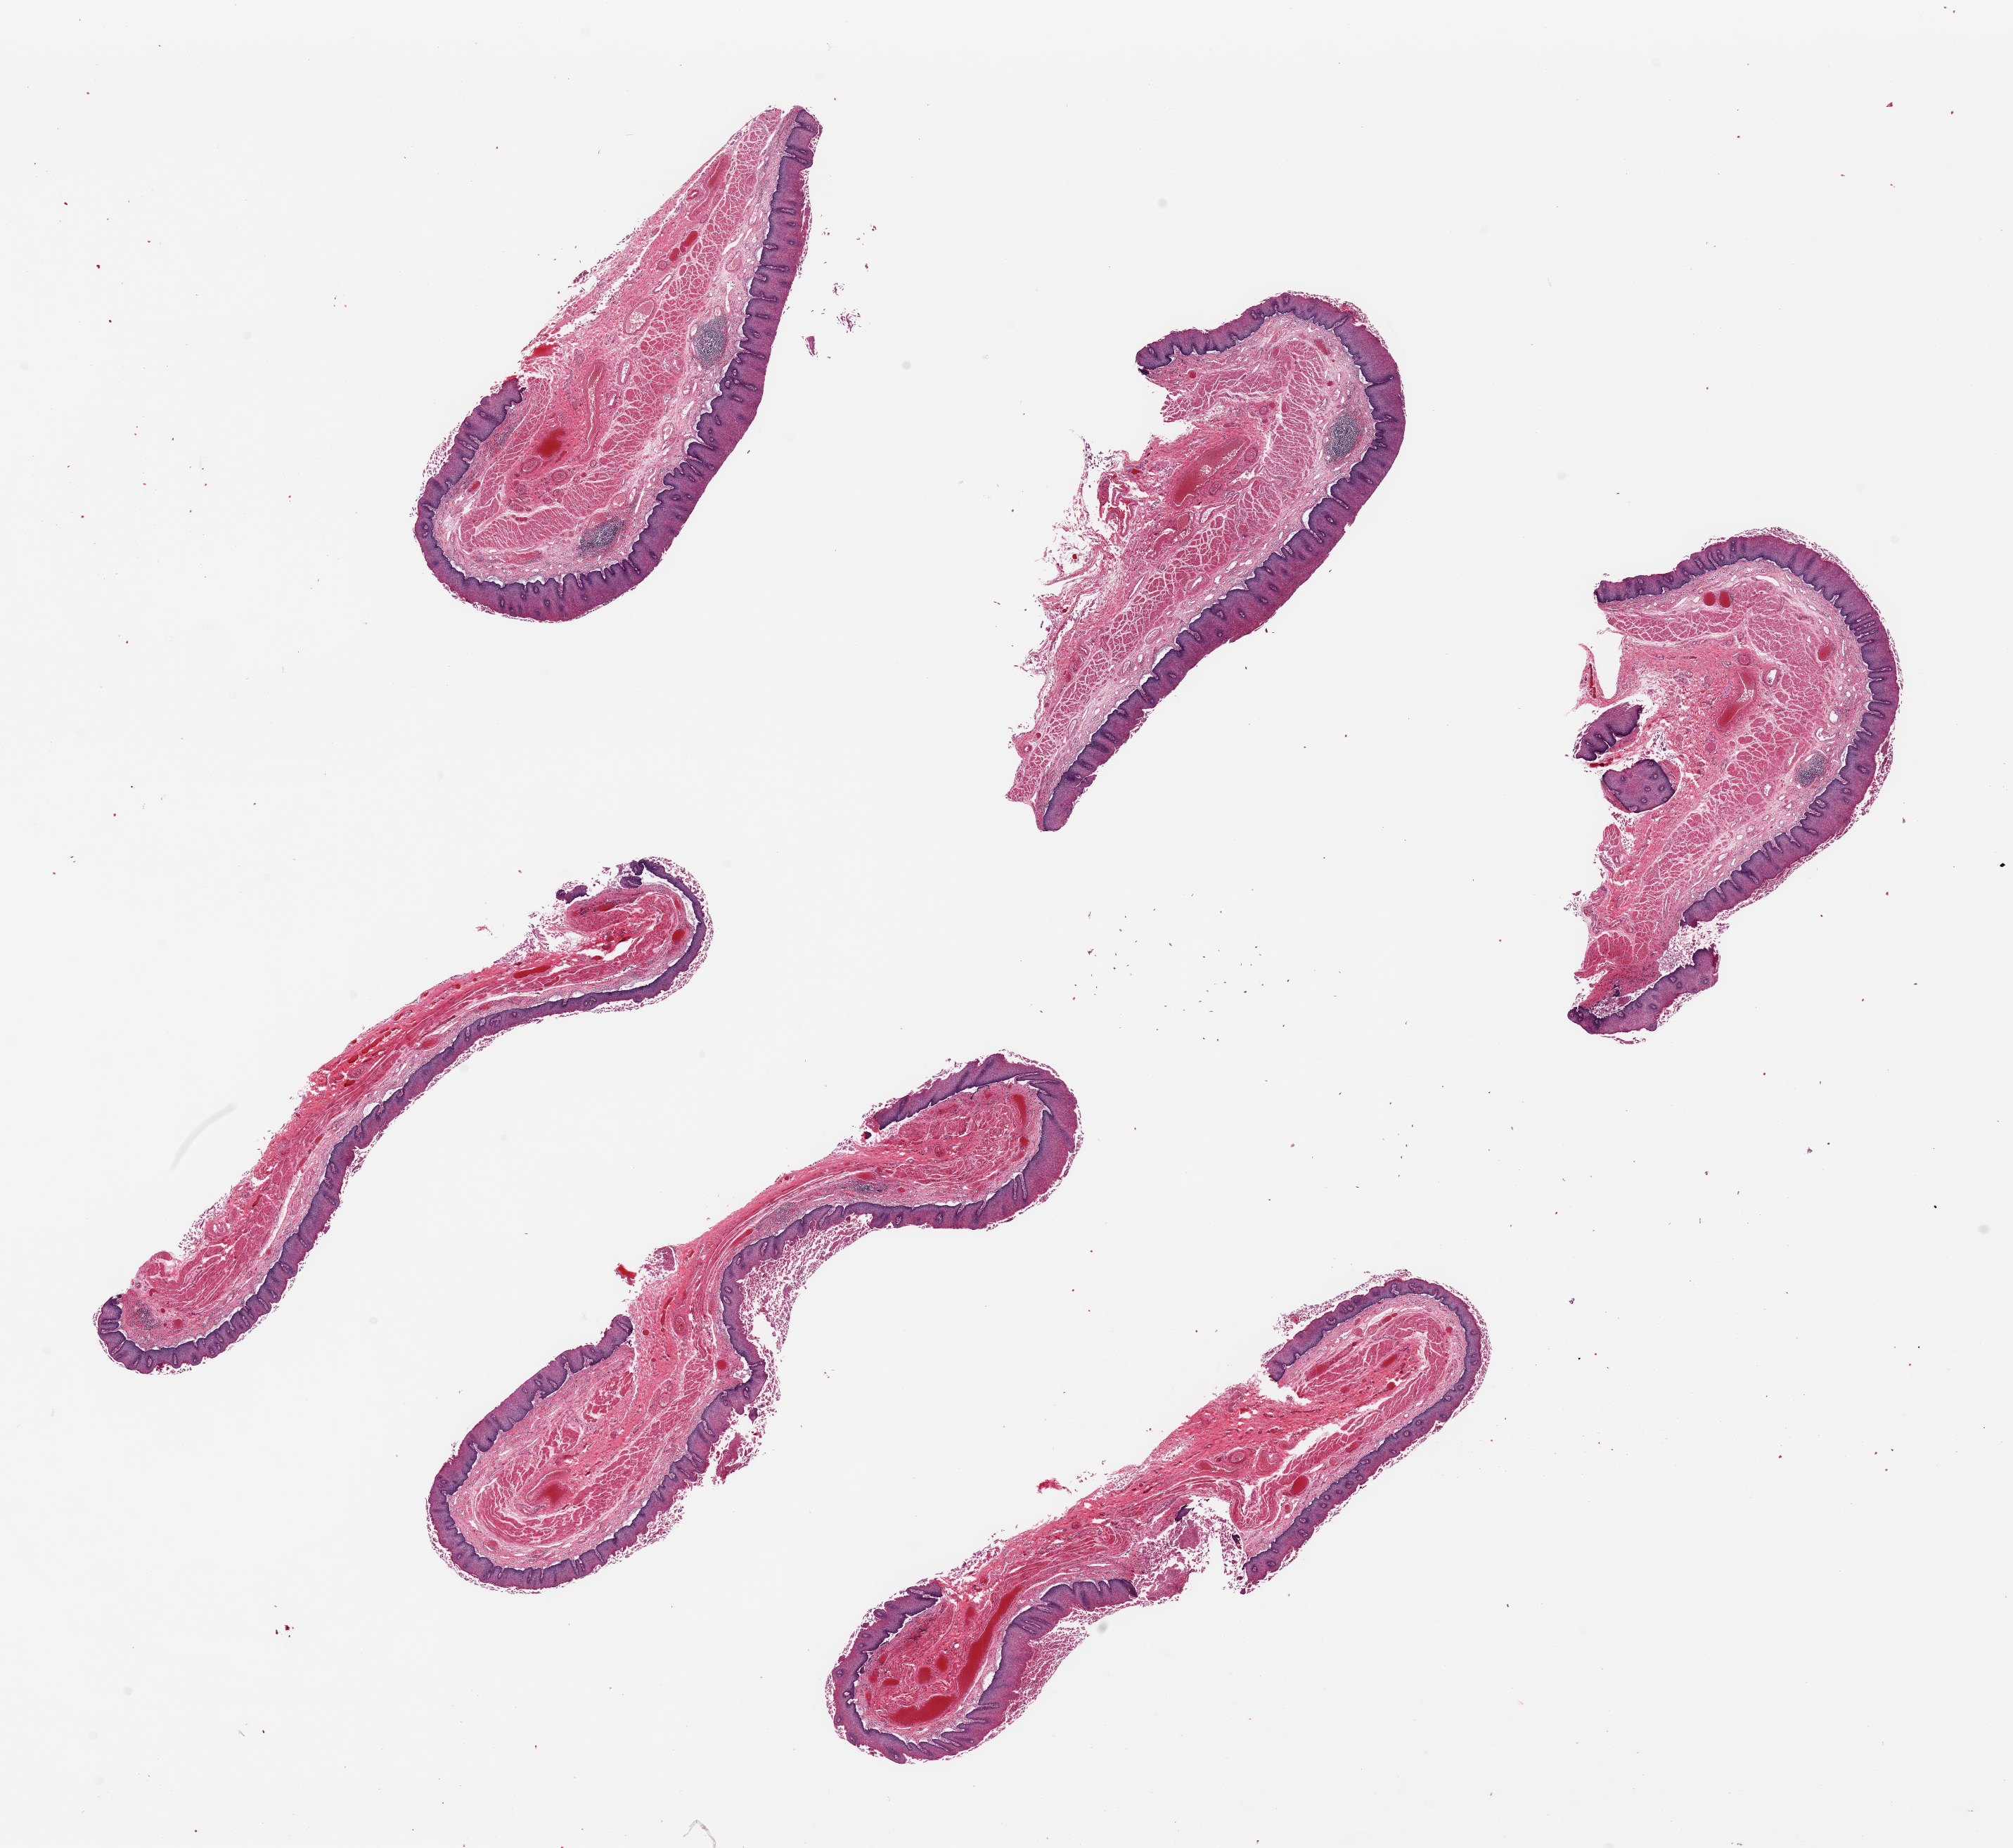
Digitized H&E-stained section — a low-resolution overview of the entire scanned area, about 22.6 x 20.8 mm (slide scanned at 20x); PAXgene-fixed paraffin-embedded (PFPE) section; target tissue: esophageal mucous membrane; donor tissue sample. Donor sex: male.
- reviewer comment on this tissue sample: 6 pieces up to 8.6x3 mm; all have mucosa not muscularis propria; re-label as Esophagus- mucosa; surface desquamation and separation of epithelium from lamina propria; possible chemical exposure